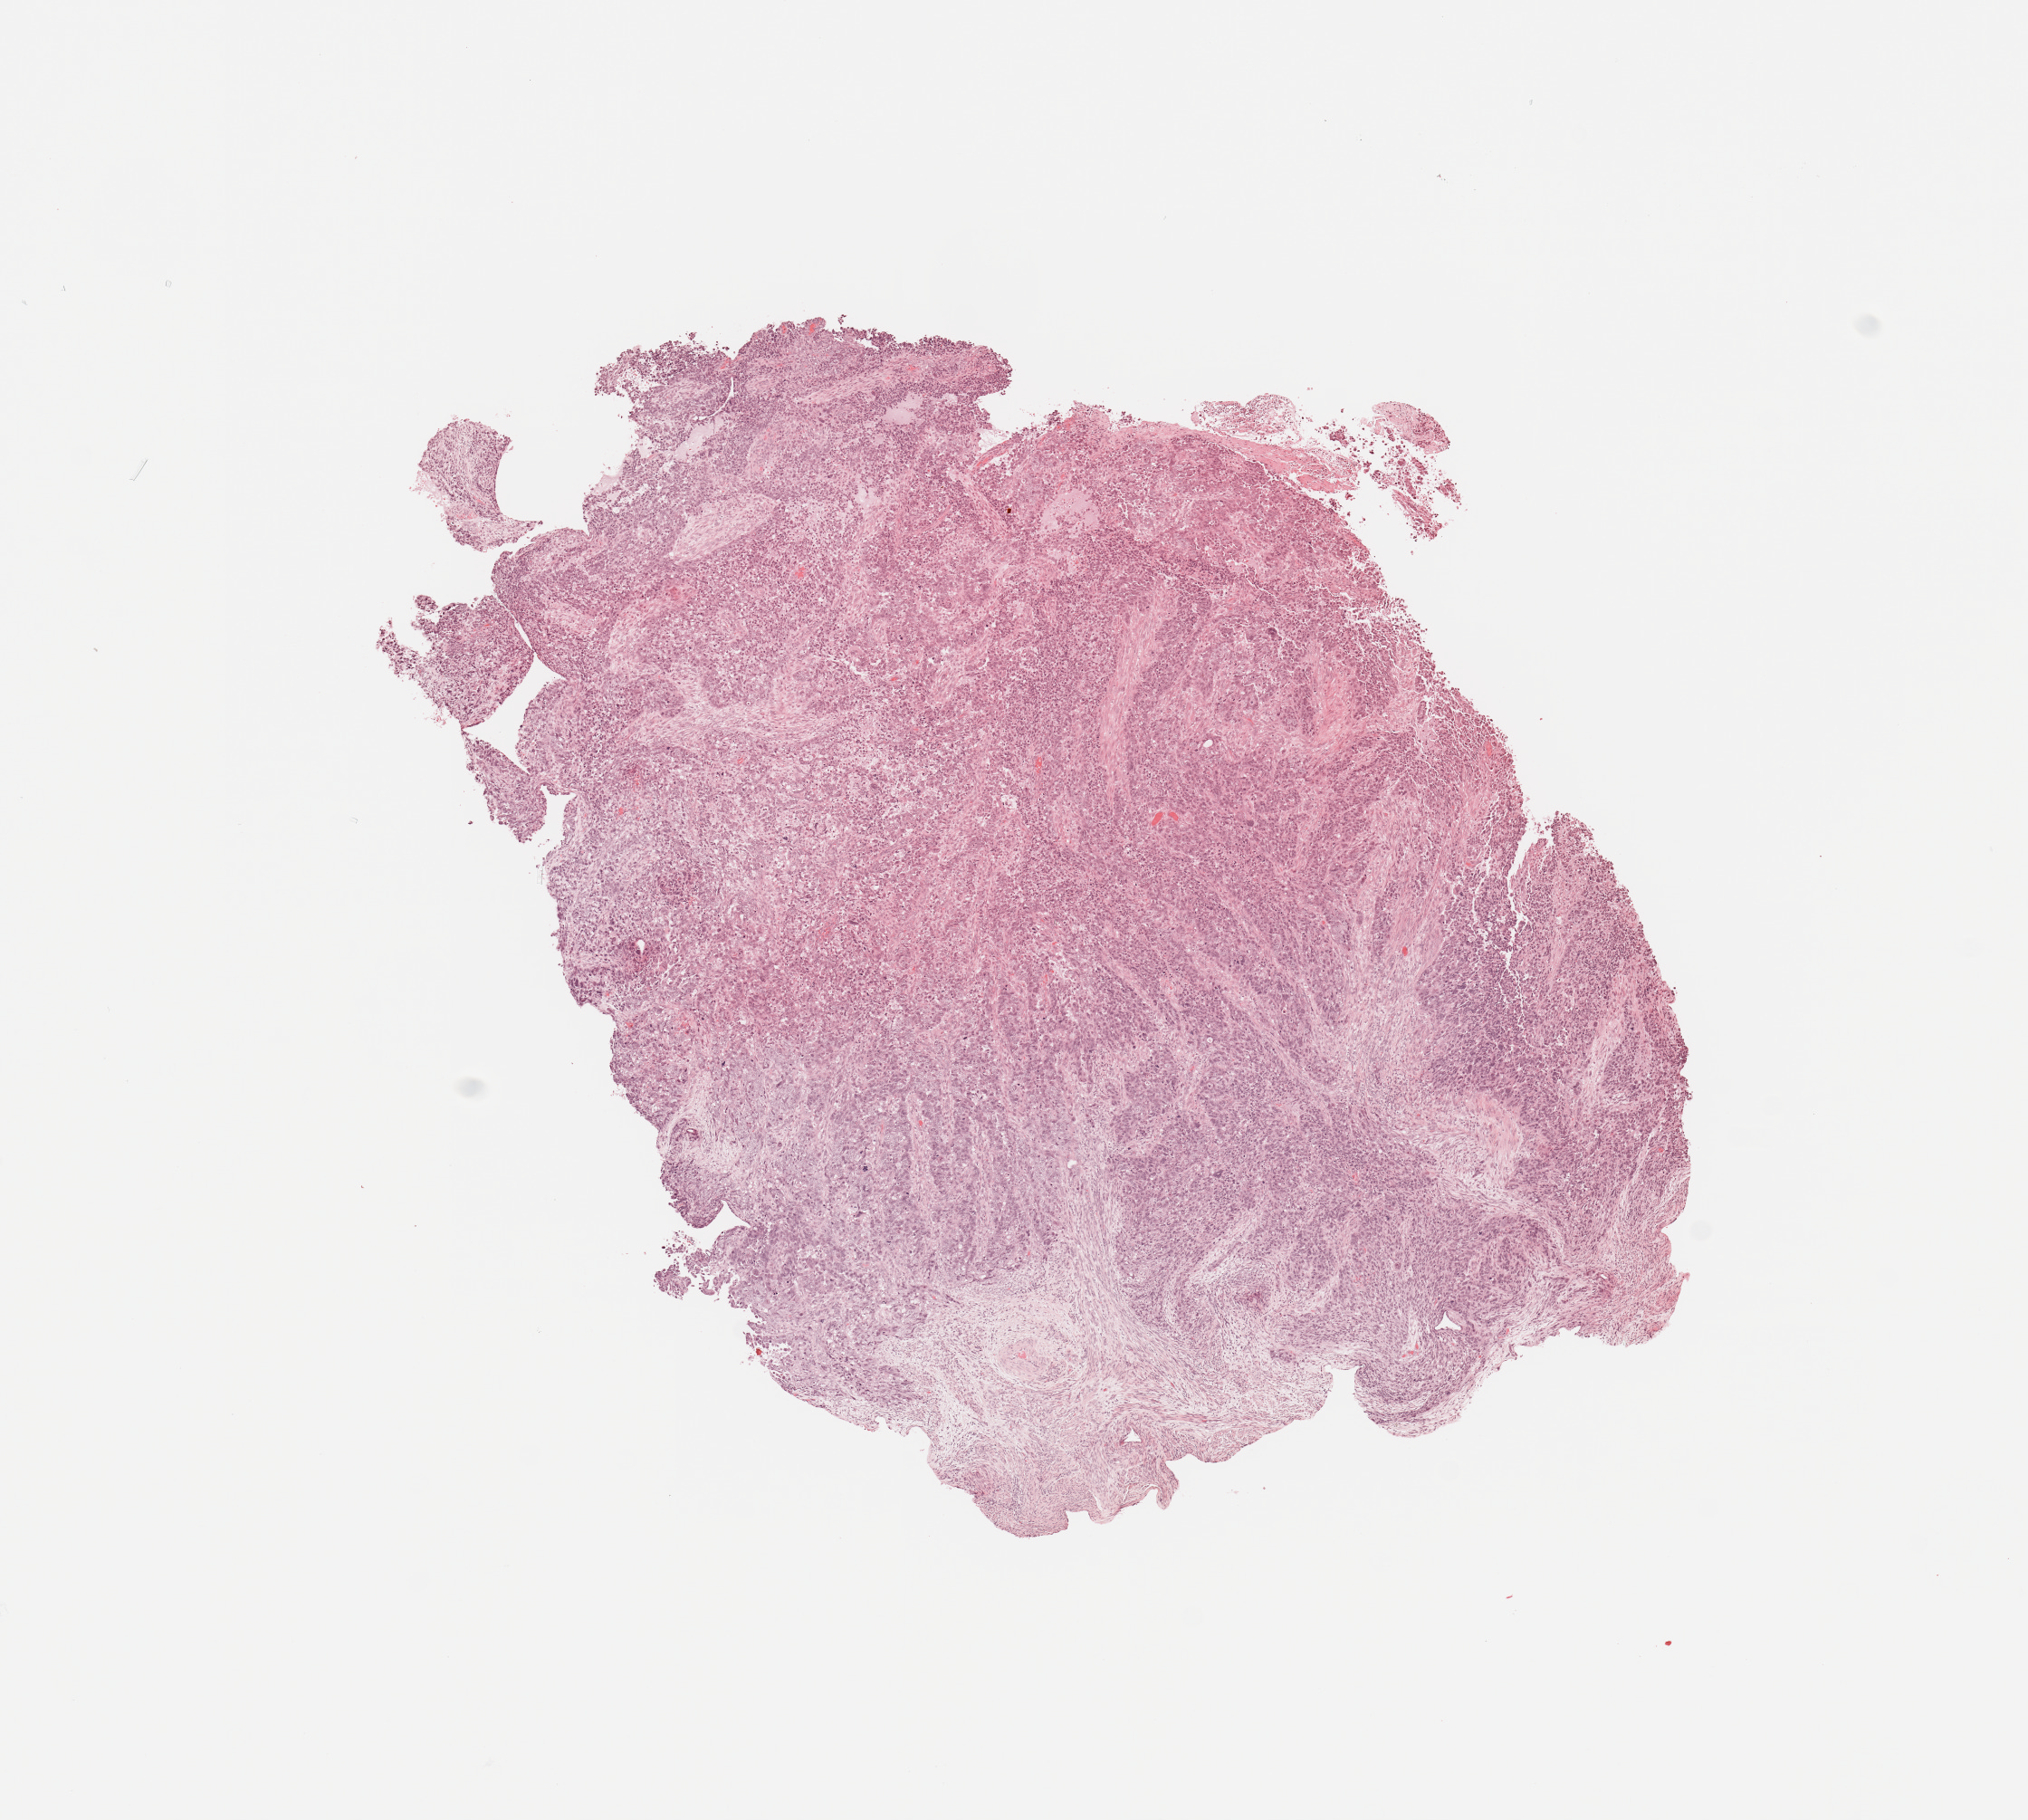
Whole-slide histology image, Hematoxylin and eosin (H&E) stained, whole scanned area (about 8.9 x 7.9 mm, acquisition: 20x scan) shown as a low-resolution overview. Tumour tissue sample, sampled site: uterus. 62-year-old female patient.
Diagnosis: Endometrioid adenocarcinoma, NOS.